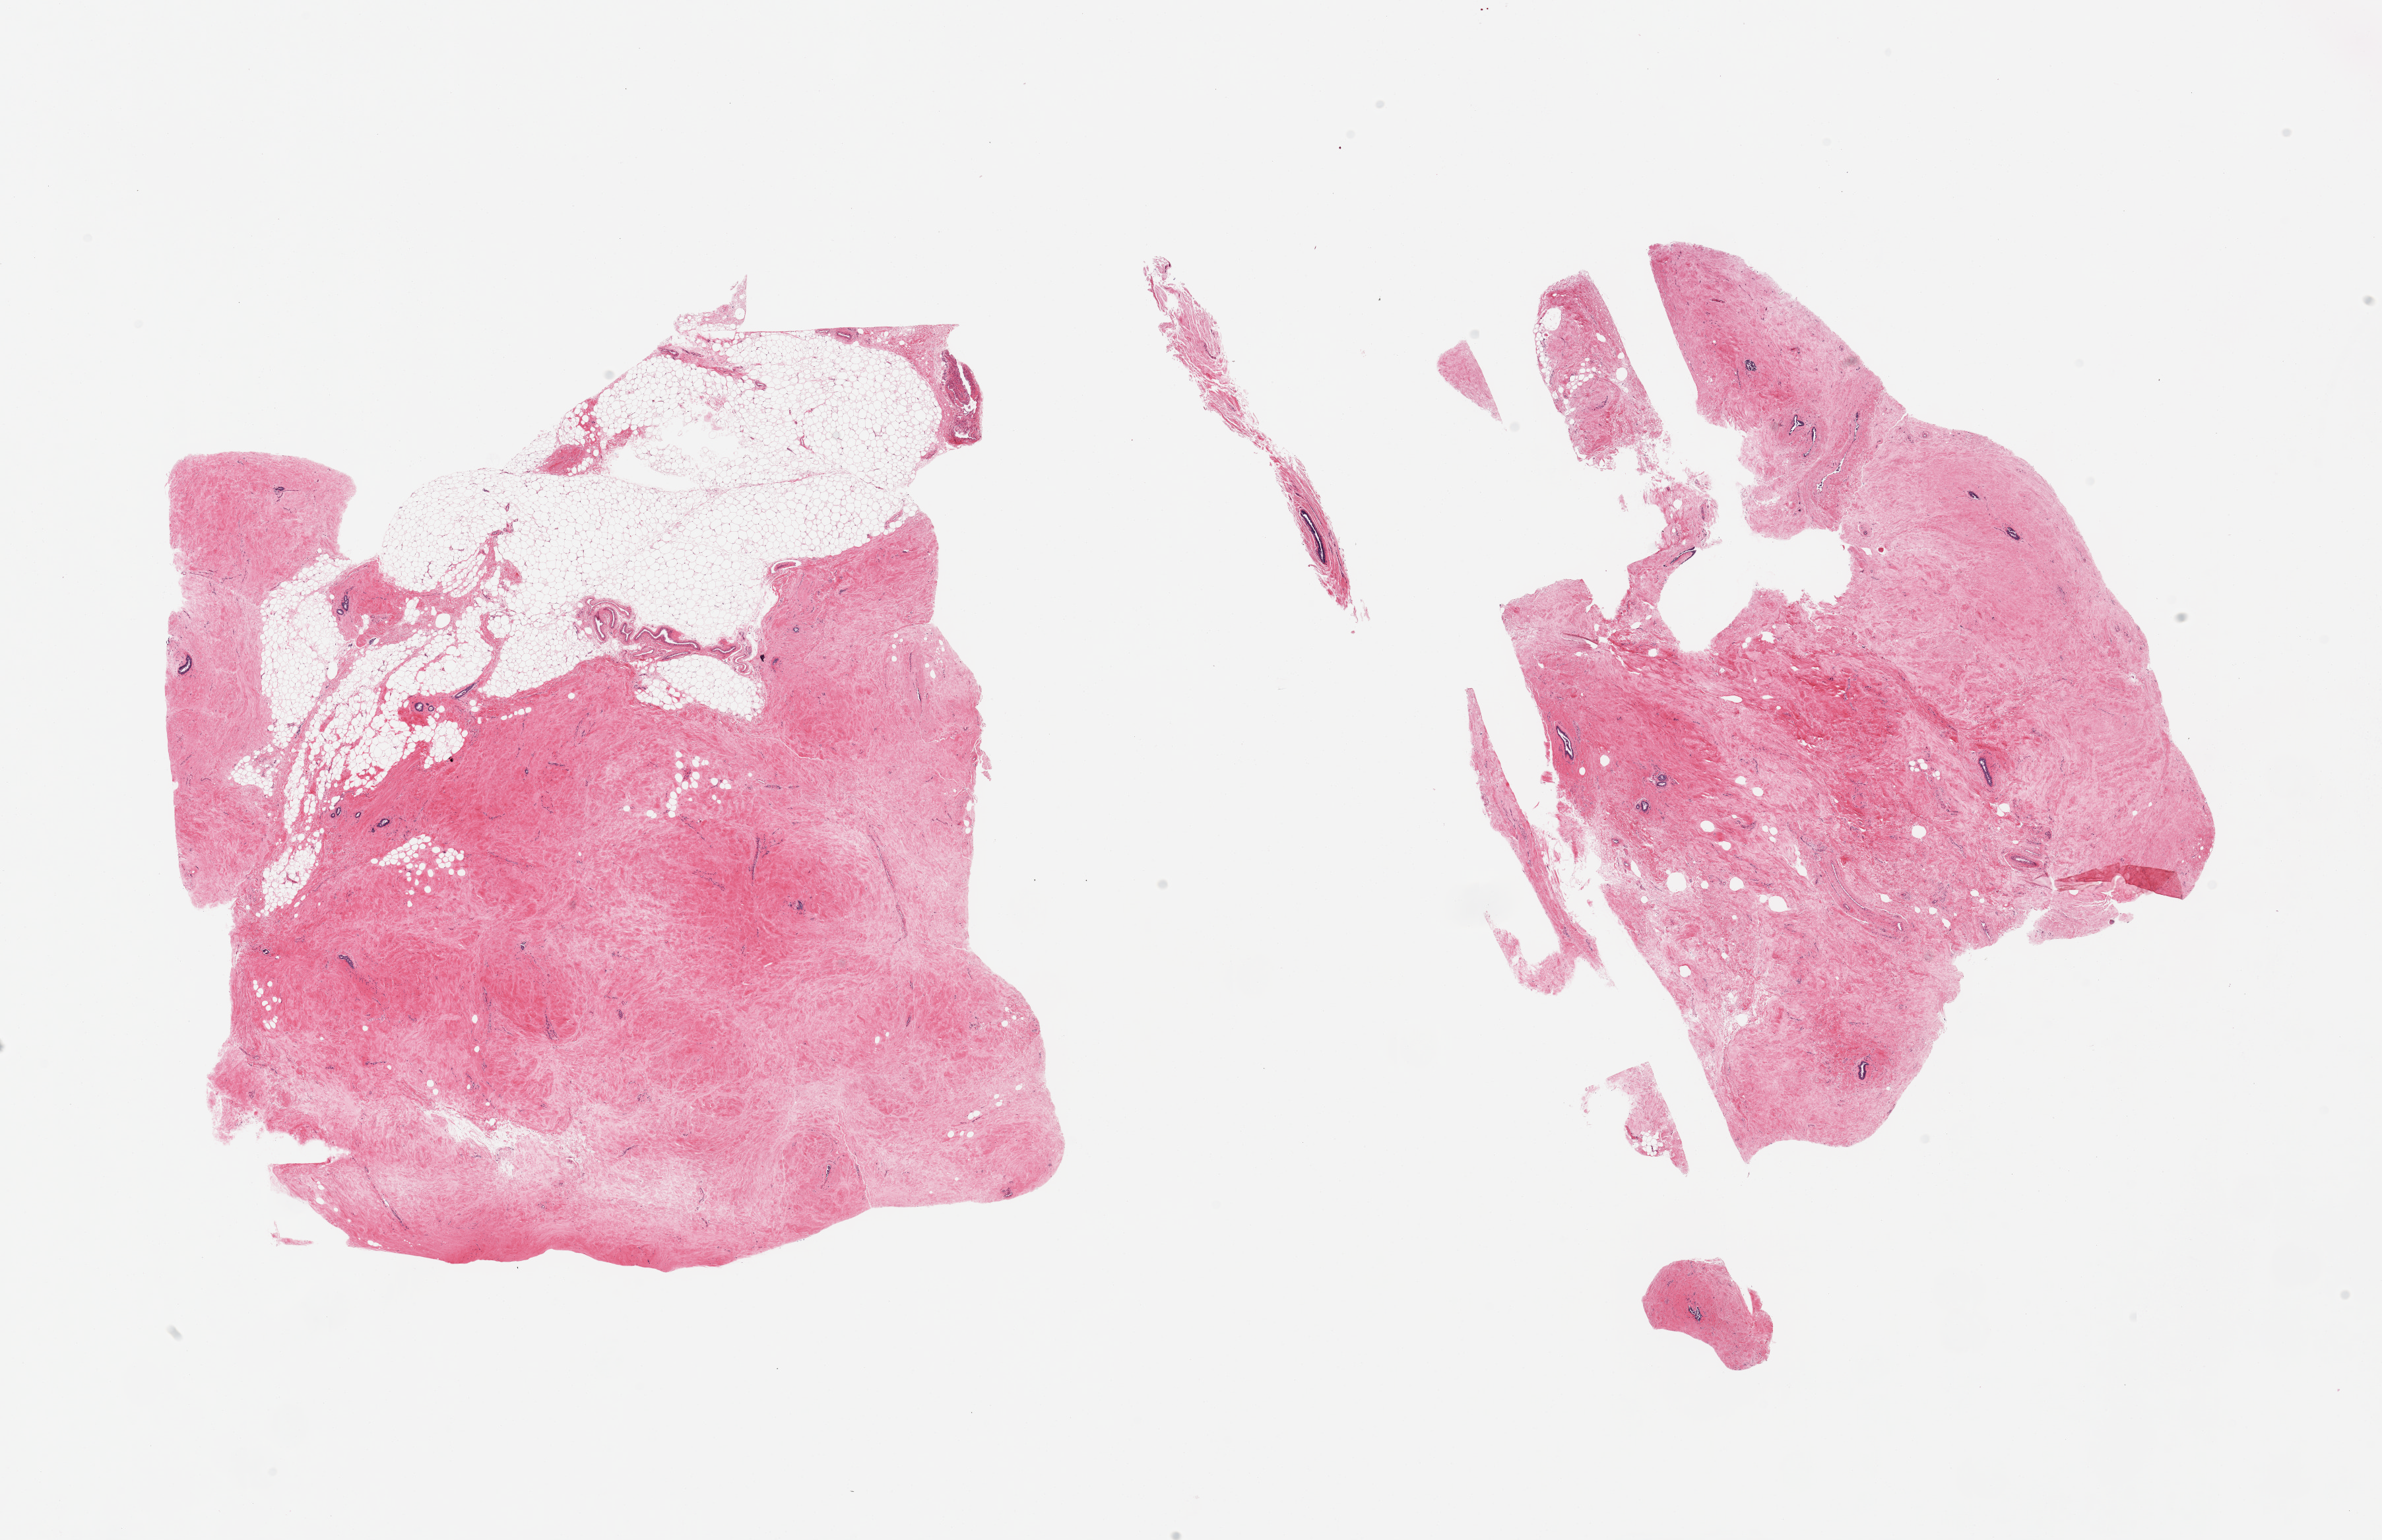
Whole-slide image, haematoxylin and eosin stain, low-resolution overview of the scanned area, about 28.5 x 18.5 mm; PAXgene-fixed, paraffin-embedded tissue; target tissue: breast; tissue donor sample.
- reviewer comment on this tissue sample: 2 pieces (1 is fragmented); predominantly fibrocollagenous stroma with sparsely scattered ductal structures, 30% of one piece is fat